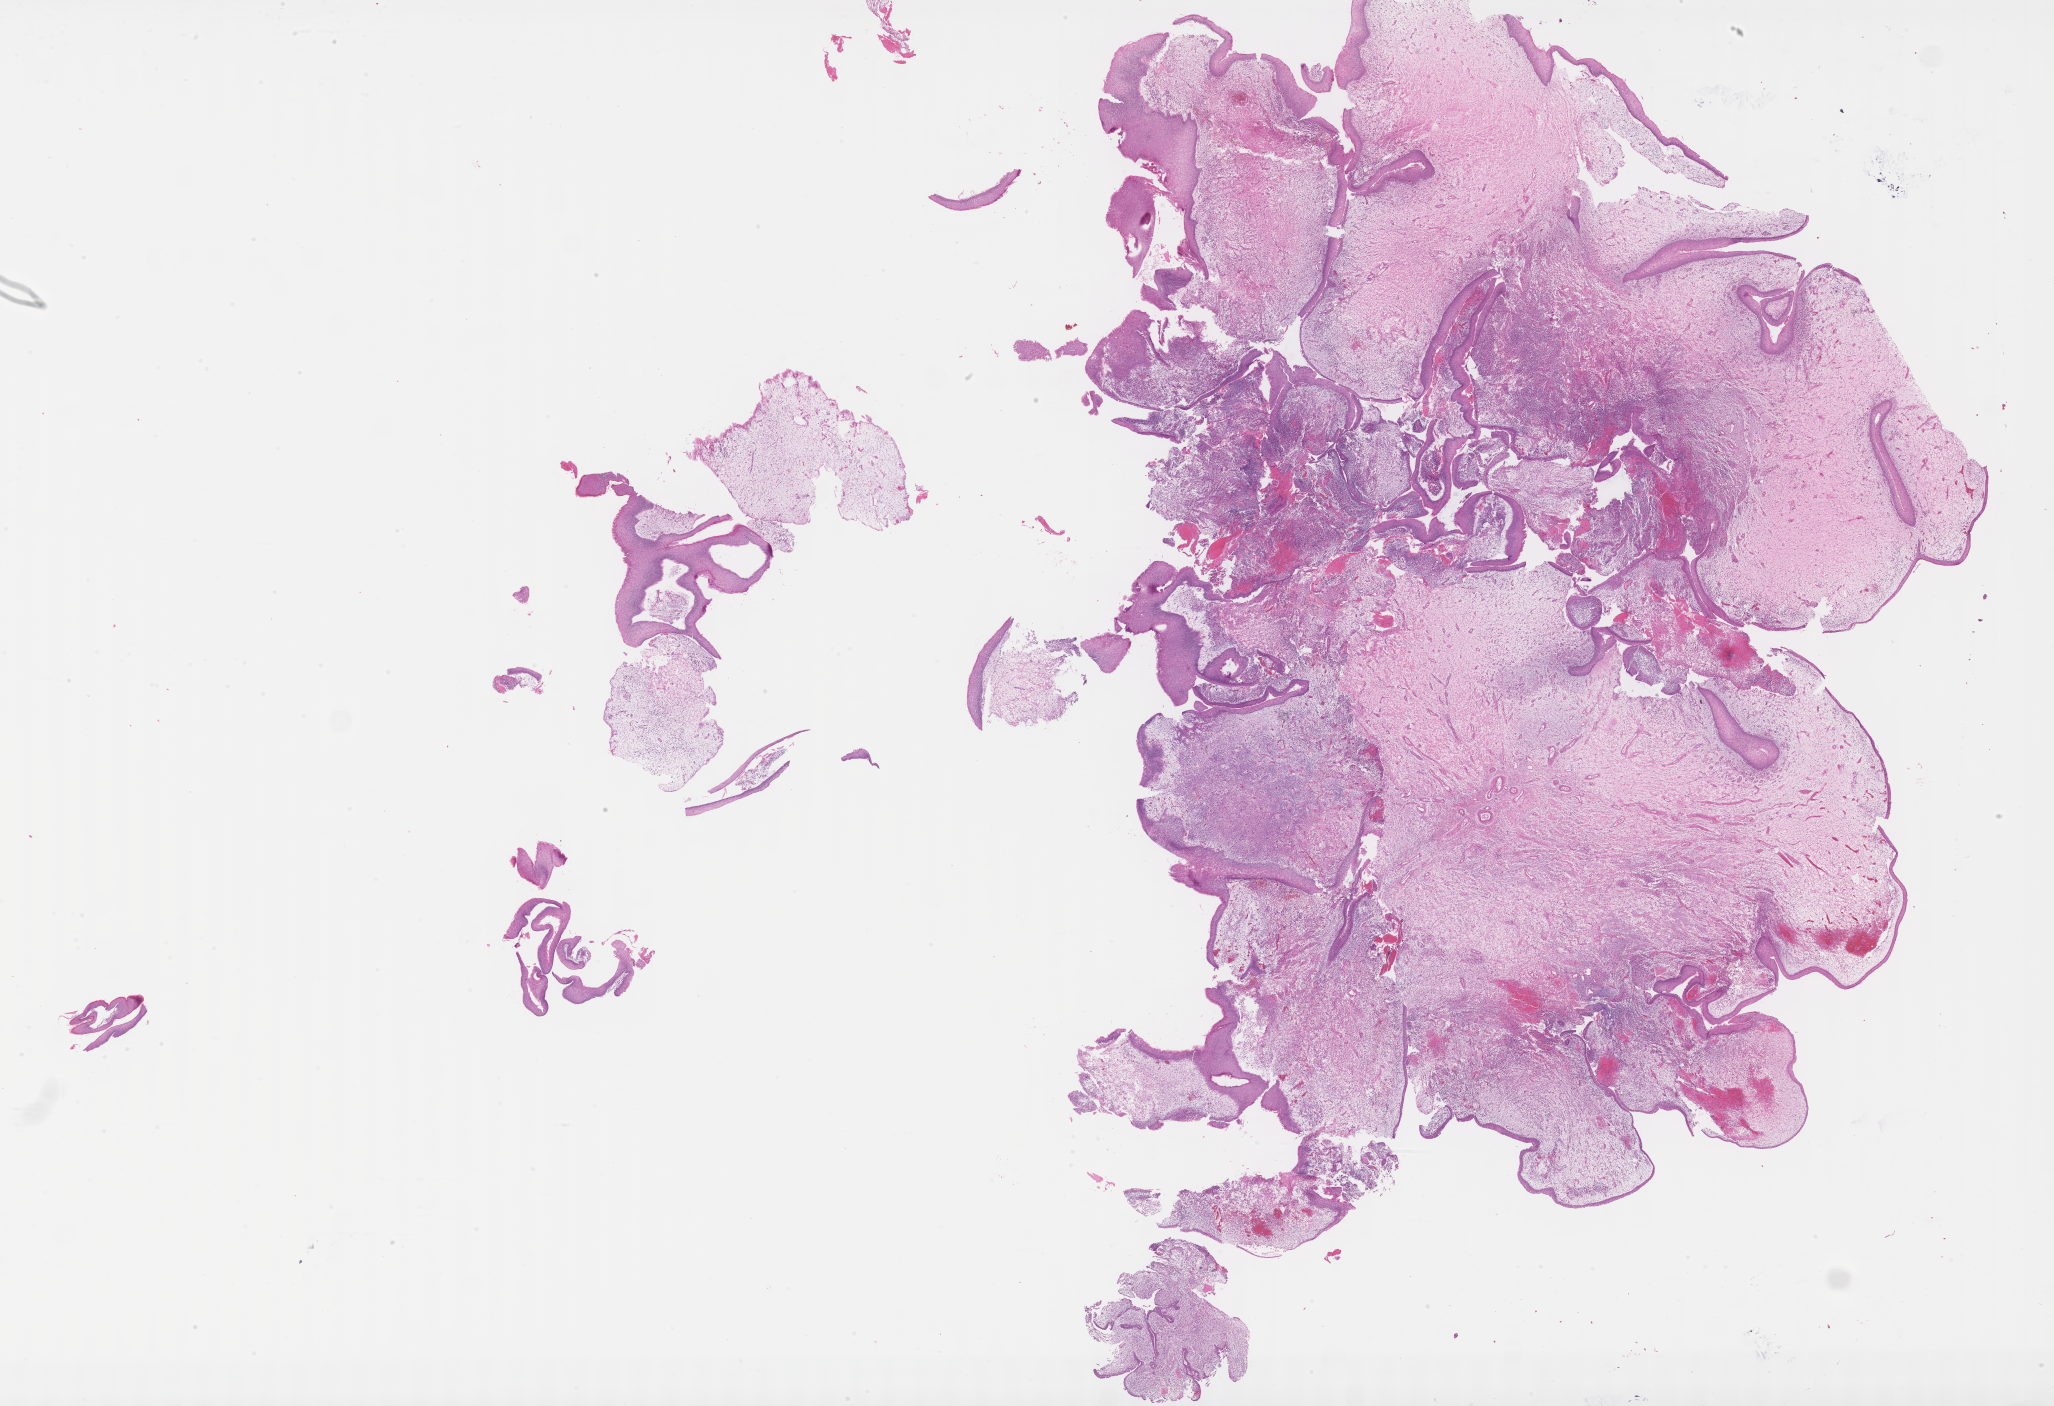
Whole-slide image, haematoxylin and eosin stain of tumor tissue — low-resolution overview of the scanned area, about 33.2 x 22.7 mm, formalin-fixed, paraffin-embedded (FFPE) tissue, site: bladder. Patient: male, age 2.1 years at diagnosis.
Diagnosis: rhabdomyosarcoma; histological classification: embryonal rhabdomyosarcoma.